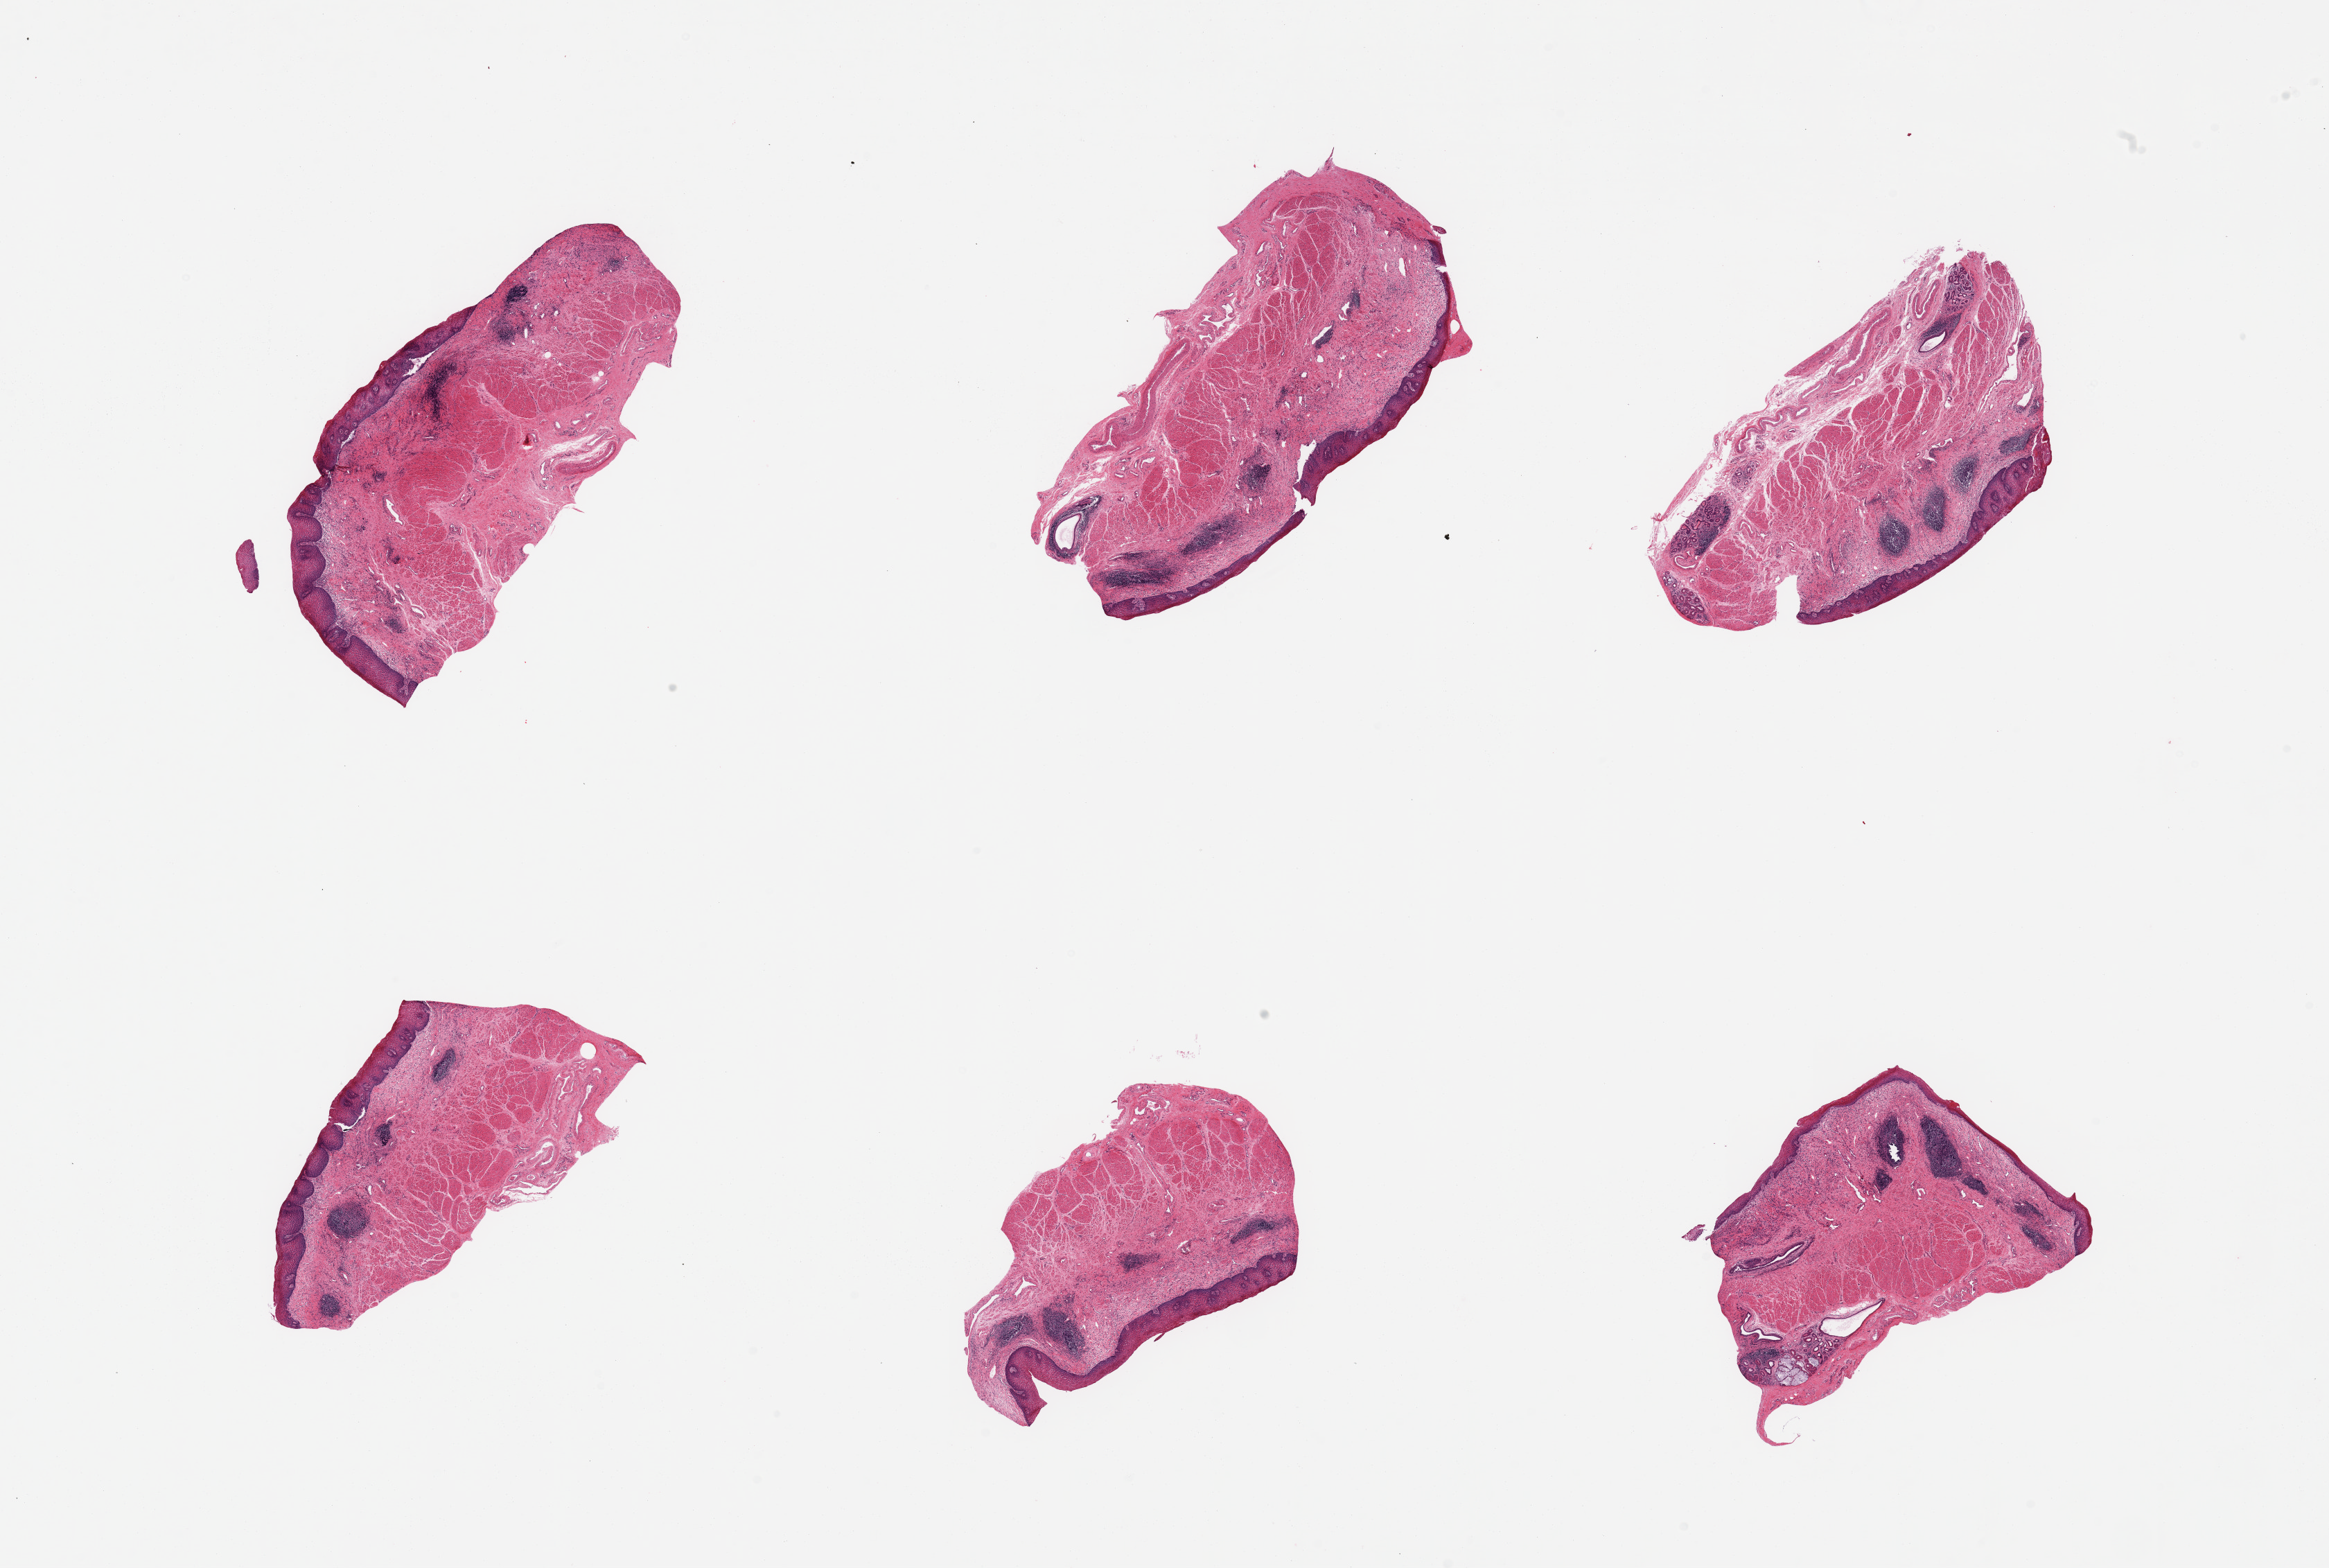
Hematoxylin and eosin (H&E) whole-slide image — shown as a low-resolution overview of the whole scanned area (about 26.6 x 17.9 mm, acquisition: 20x scan). PAXgene-fixed, paraffin-embedded tissue. Target tissue: esophageal mucous membrane. Tissue donor sample. Male donor.
Reviewer comment on this tissue sample: 6 pieces, squamous mucosa up to ~0.4mm, ~15-20% thickness.